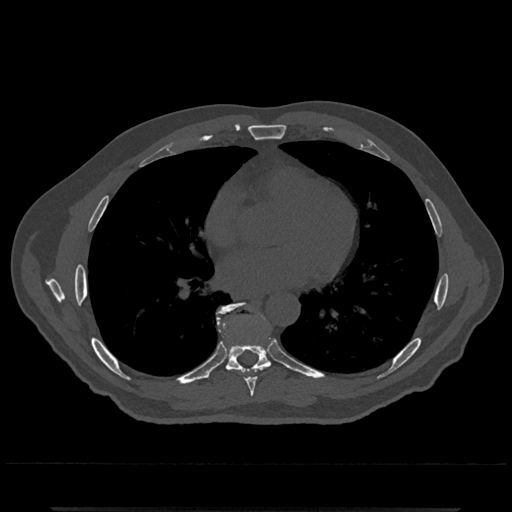
CT including the spine, one axial slice; position 693 of 797 along the scan axis; 120 kVp; bone window (W 1800 / L 400 HU); 0.5 mm slice thickness; 512 × 512 image matrix, field of view 393 × 393 mm. Patient: male, 67 years. From the clinical record (not read from this slice): primary cancer: prostate.
Structures marked on this image (semi-automatically segmented with operator editing):
- T7 vertebra: bounding box <225,365,271,397> (left, top, right, bottom; pixels)
- T8 vertebra: <216,302,271,374>